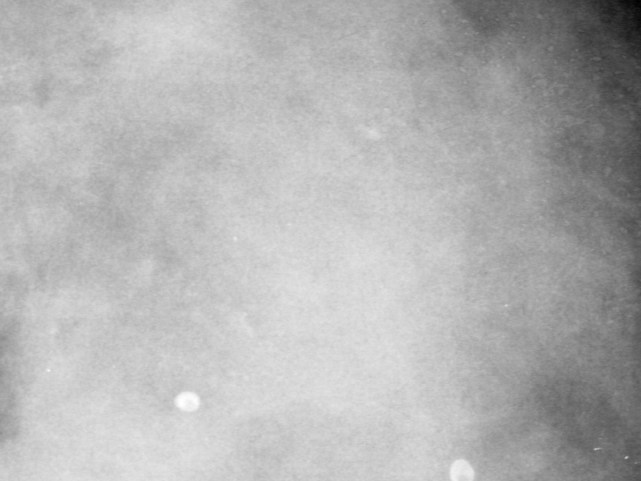
Cropped region of a digitized screen-film mammogram centred on a radiologist-marked abnormality, right breast, MLO view, BI-RADS breast density category 4 (scale 1–4).
- Calcifications, morphology punctate, distribution segmental; BI-RADS assessment category 4; subtlety rating 1 on a 1 (subtle) to 5 (obvious) scale; pathology result (as recorded, not read from the image): benign.